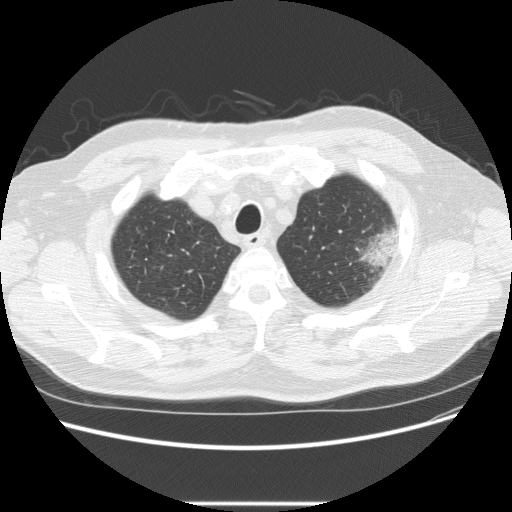
Axial slice from a low-dose chest CT screening exam; baseline screening round; lung window (W 1500 / L -600 HU); standard (soft-tissue) reconstruction kernel (STANDARD); 120 kVp. Male, age 73 years at enrolment. Former smoker at enrolment.
- Expert reader's lesion annotation, bounding box (x1, y1, x2, y2) in pixels: (332, 216, 407, 283).
- The screening reader recorded 2 non-calcified nodules or masses ≥4 mm on this exam (left upper lobe, right upper lobe); which of them this box marks is not recorded.
- Official screen result: positive, change unspecified: nodule(s) >= 4 mm or enlarging nodule(s), mass(es), or other non-specific abnormalities suspicious for lung cancer.
- Lung cancer was diagnosed 11 days after this screen: bronchiolo-alveolar adenocarcinoma, NOS, other location, well differentiated (G1), stage IV (AJCC 6th edition).